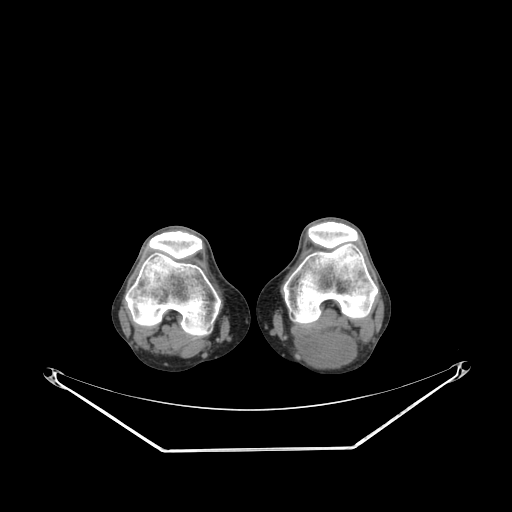
CT of an extremity soft-tissue mass (from a PET/CT study), one axial slice. Slice 179 of 267 in the series (ordered by position). Reconstruction kernel SOFT. Soft-tissue window (W 400 / L 40 HU). 3.75 mm slice thickness. 512 × 512 image matrix, field of view 500 × 500 mm. Male patient. Case-level facts recorded for this patient, not image findings: histological type: synovial sarcoma; site of the primary tumour: left poplietal fossa.
Outlined on this slice (expert contour drawn on MRI and transferred to this co-registered scan by the dataset authors):
- gross tumour volume (mass): box from (x=294, y=329) to (x=357, y=368) px